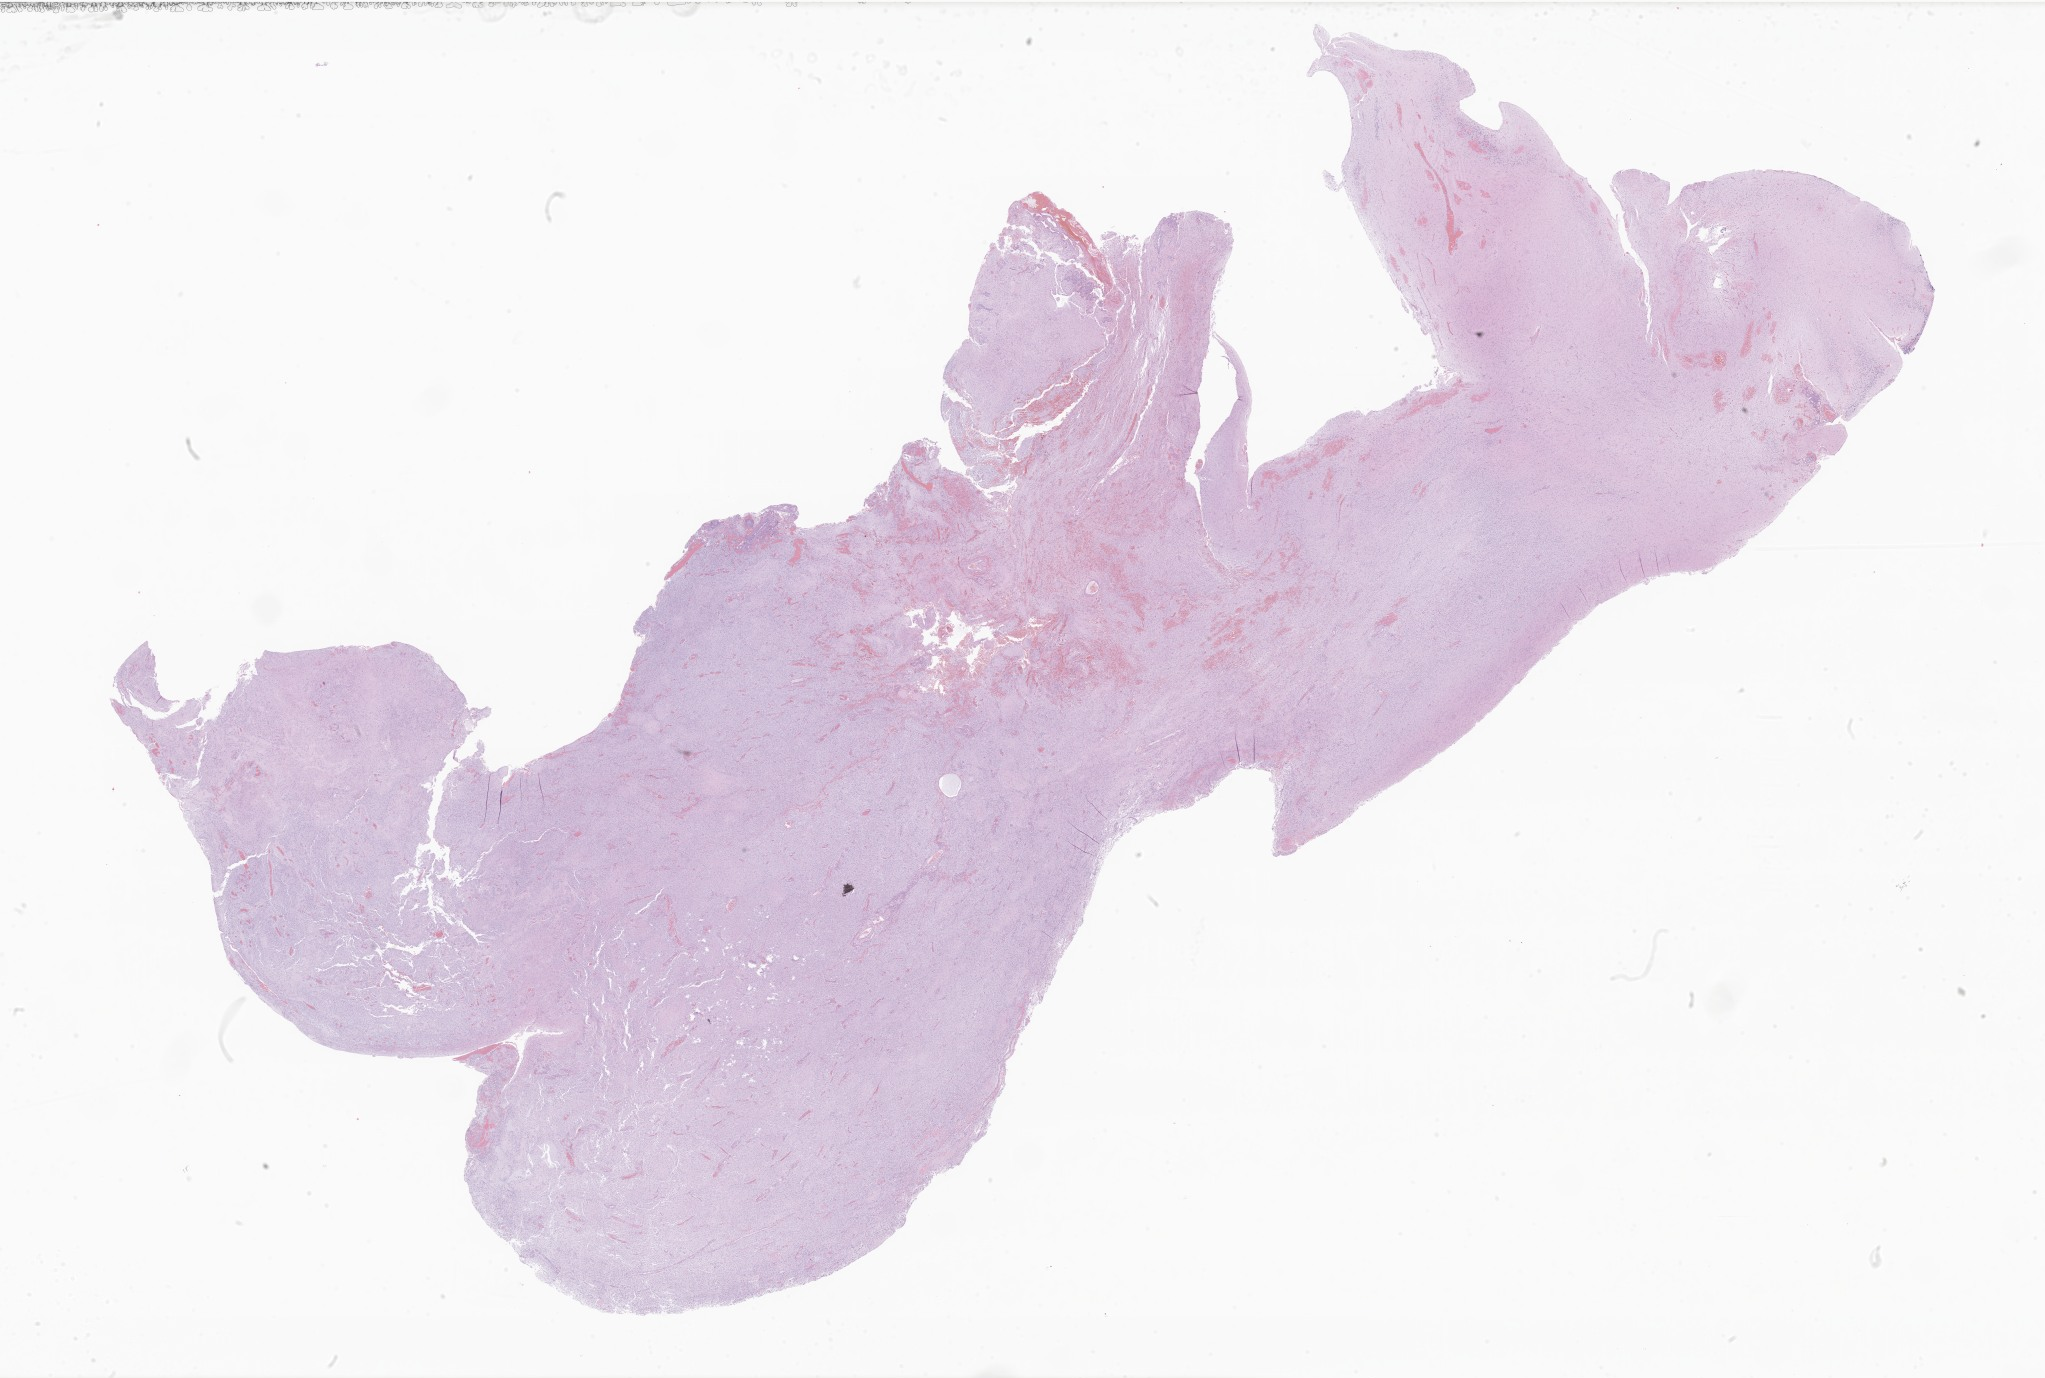
Hematoxylin and eosin (H&E) whole-slide image of tumor tissue from the brain, shown as a low-resolution overview of the whole scanned area (about 34.5 x 23.2 mm), formalin-fixed paraffin-embedded section. Patient male; age 110 months (9 years 2 months).
Diagnosis: Neoplasm, uncertain whether benign or malignant.